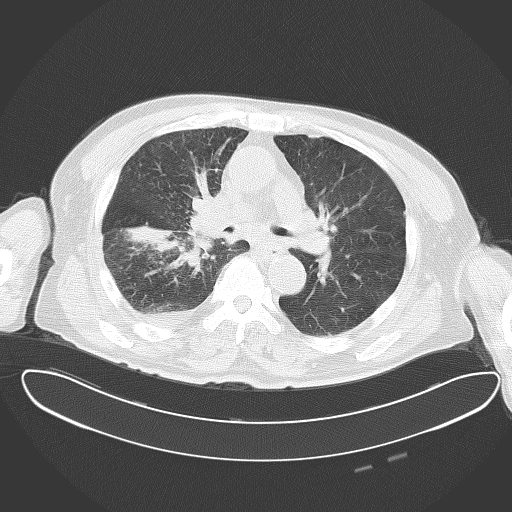
Chest CT, one axial slice. 120 kVp. Lung window (W 1500 / L -600 HU). 5 mm slice thickness. 512 × 512 image matrix. Patient: male, 78 years. From the clinical record (not read from this slice): clinical TNM (as recorded): T2 N1 M1.
Structures marked on this image (rectangle marked by the reading radiologist):
- lung tumour (recorded histology: adenocarcinoma): bounding box [x1, y1, x2, y2] px = [118, 183, 237, 280]